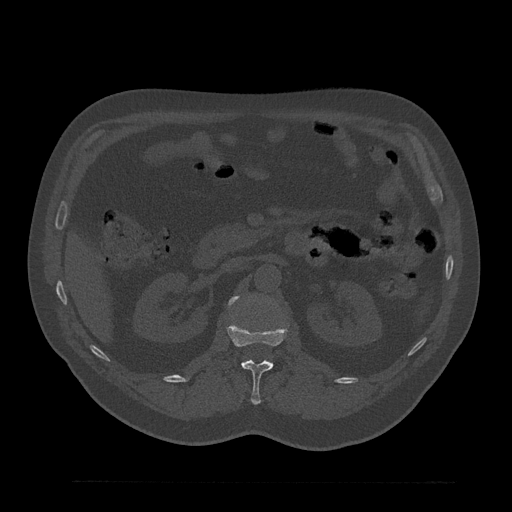
CT including the spine, one axial slice; position 150 of 797 along the scan axis; bone window (W 1800 / L 400 HU); 0.5 mm slice thickness; 512 × 512 image matrix, field of view 430 × 430 mm. Male patient, age 61 years. Case-level facts recorded for this patient, not image findings: primary cancer: prostate.
Structures marked on this image (semi-automatically segmented with operator editing):
- L1 vertebra: bounding box <226,321,287,405> (left, top, right, bottom; pixels)
- L2 vertebra: <228,296,238,305>